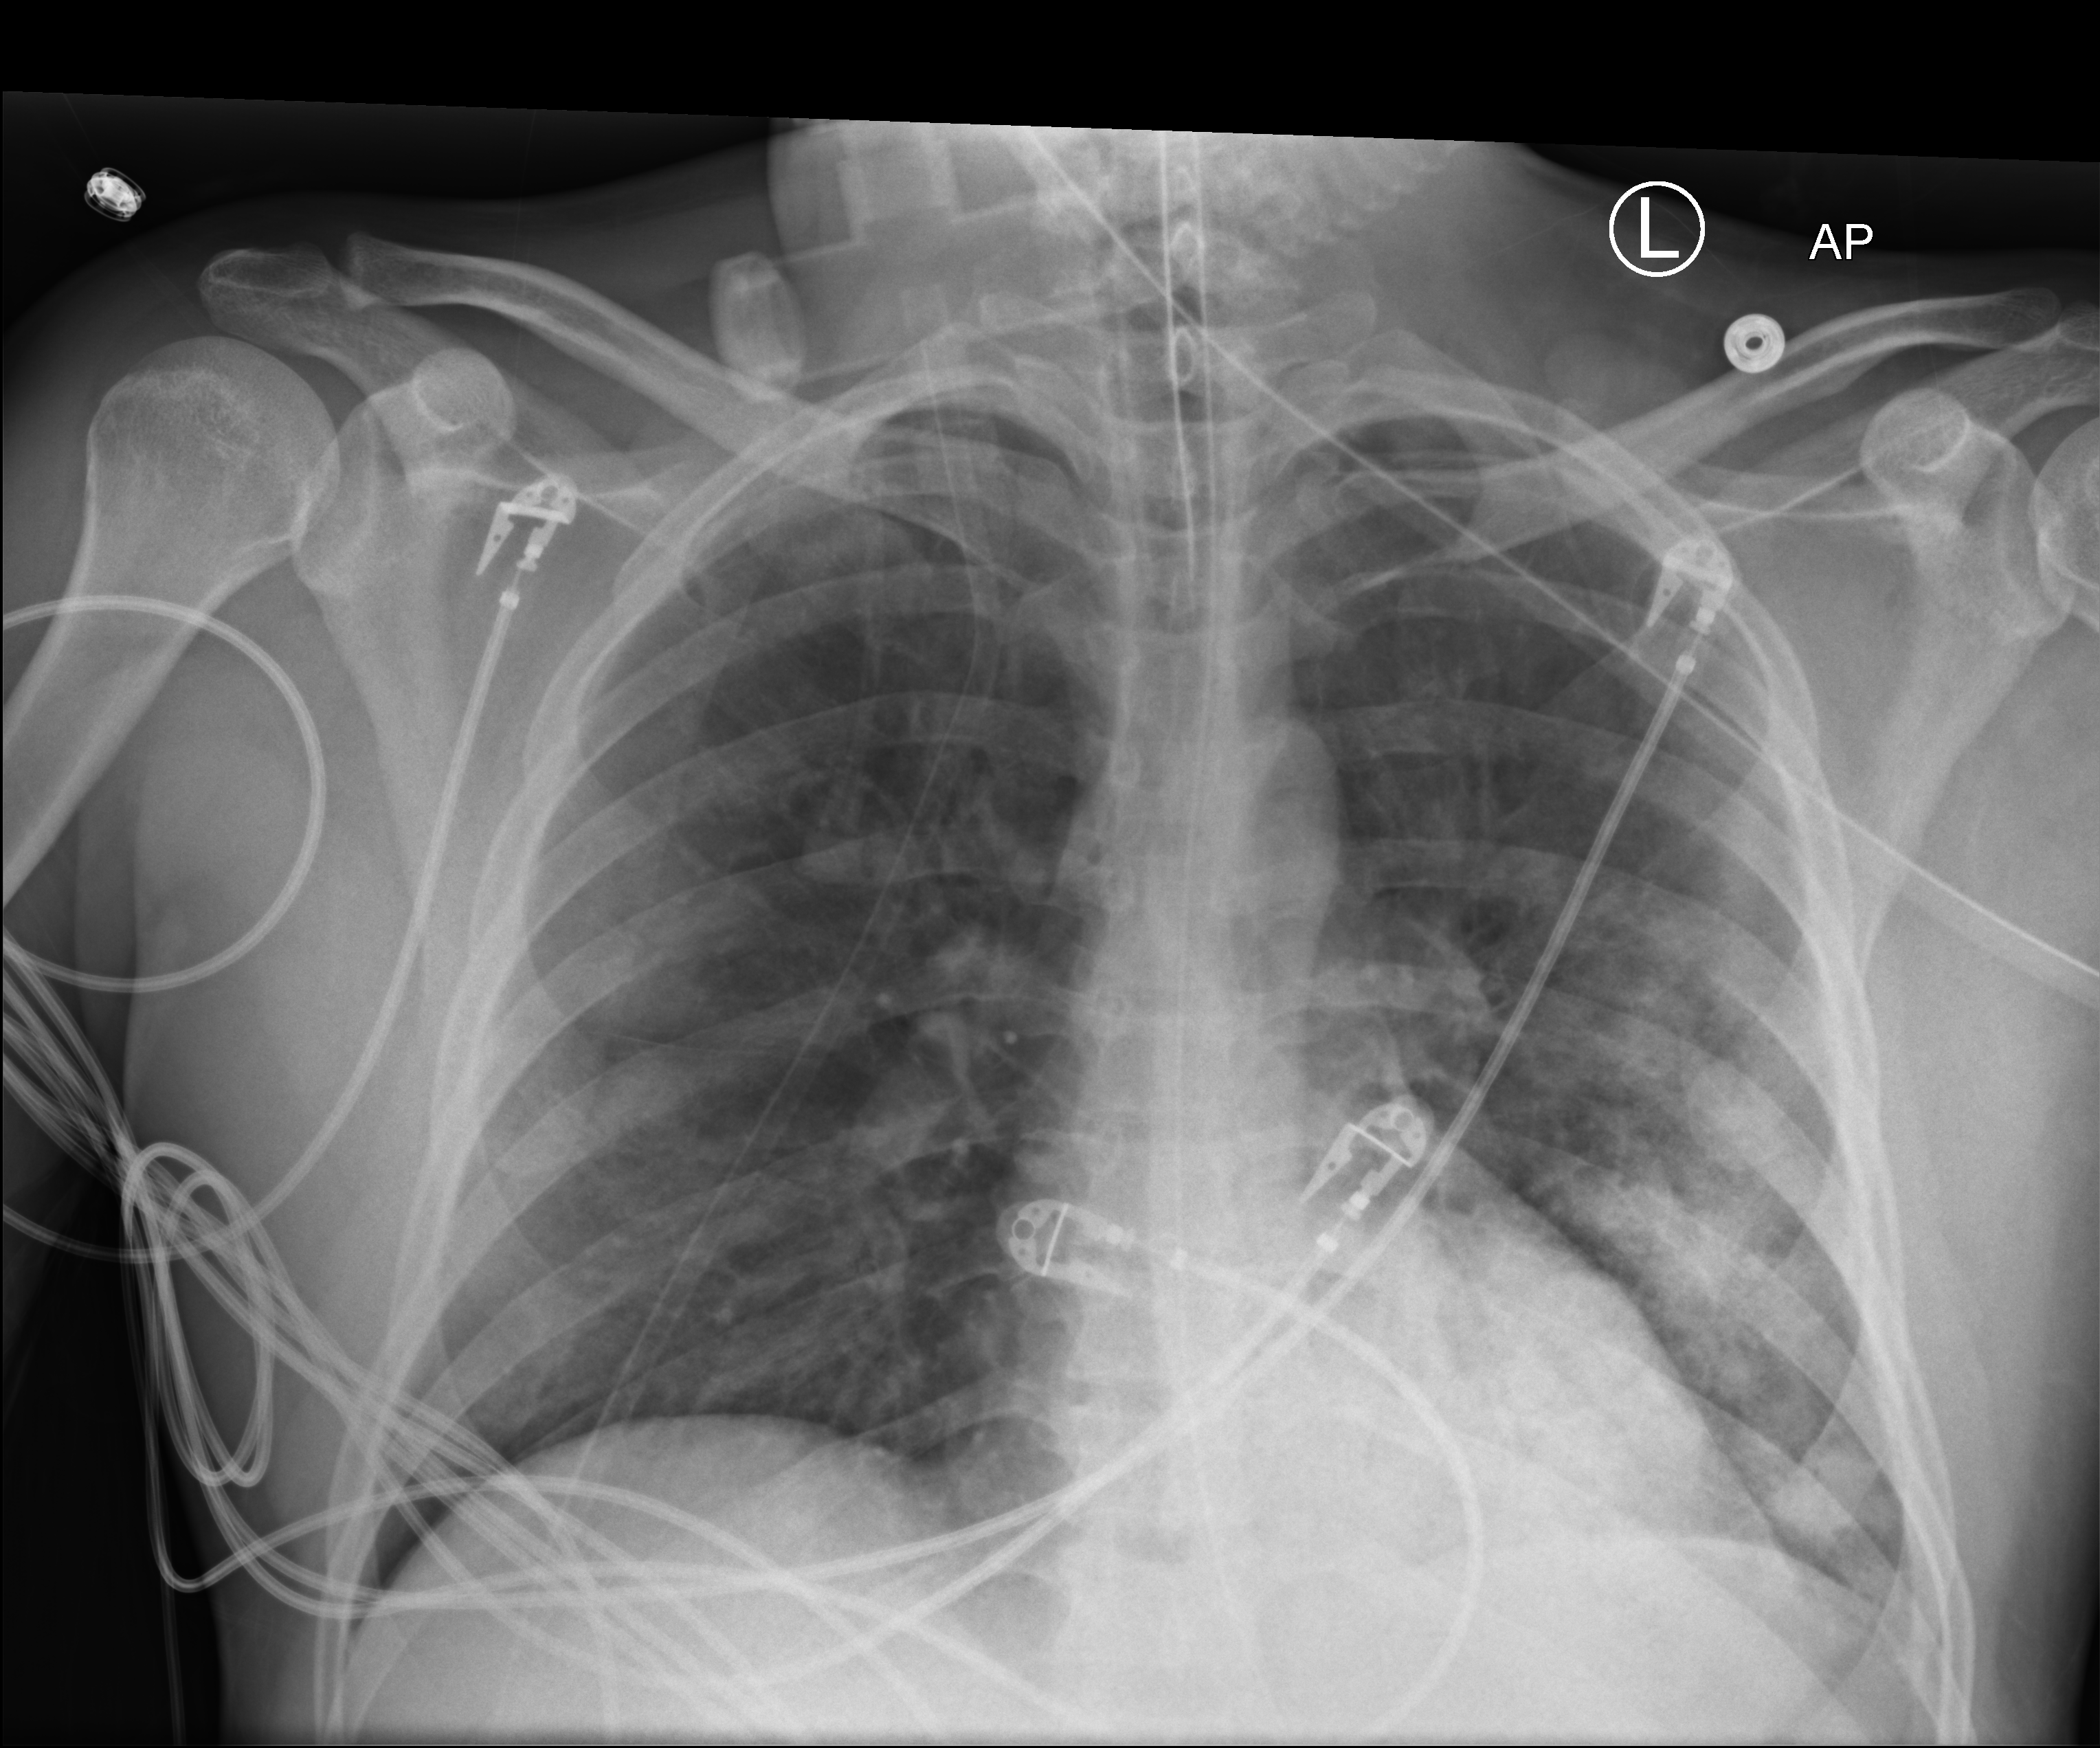
Bedside chest radiograph (computed radiography); anteroposterior (AP) projection. Male patient hospitalised with COVID-19, age 18–59 years.
From the hospital-stay record, not from the radiograph (when in the stay this image was taken is not recorded): smoking status (admission record): never; admitted to intensive care during this hospital stay: yes.